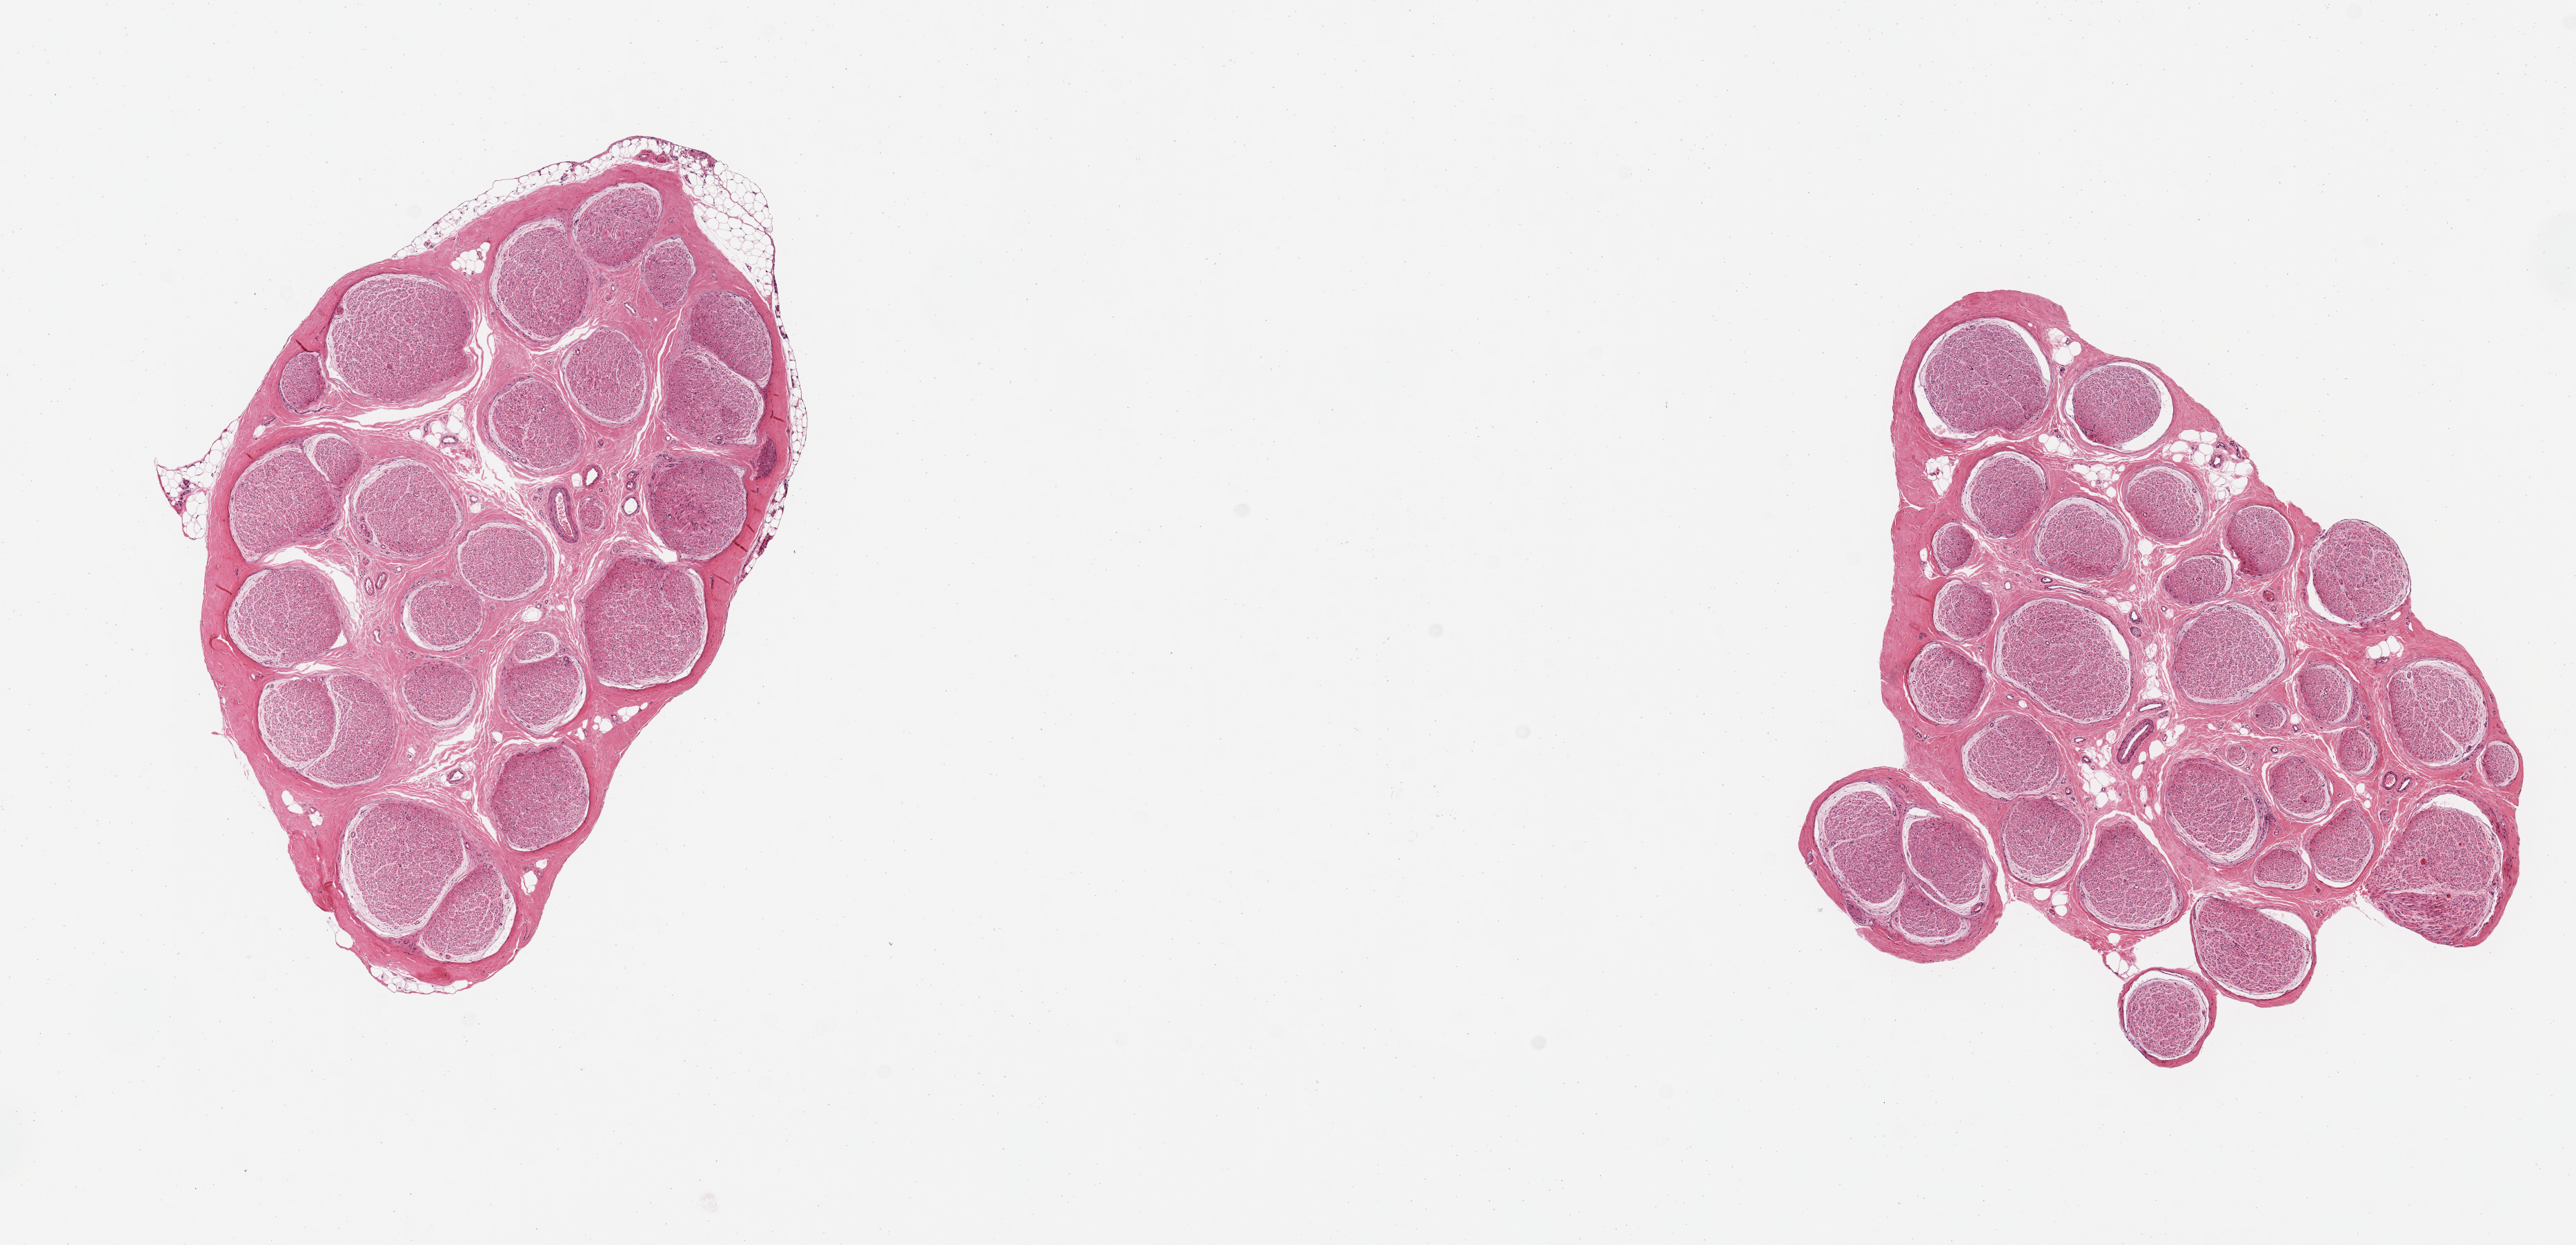
Digitized haematoxylin and eosin-stained section, whole scanned area (about 14.8 x 7.1 mm, acquisition: 20x scan) shown as a low-resolution overview; PAXgene-fixed, paraffin-embedded tissue; target tissue: tibial nerve; tissue donor sample.
Pathologist's review note for this sample: 2 pieces, good clean sections; trace rim of fat, ~0.4mm.